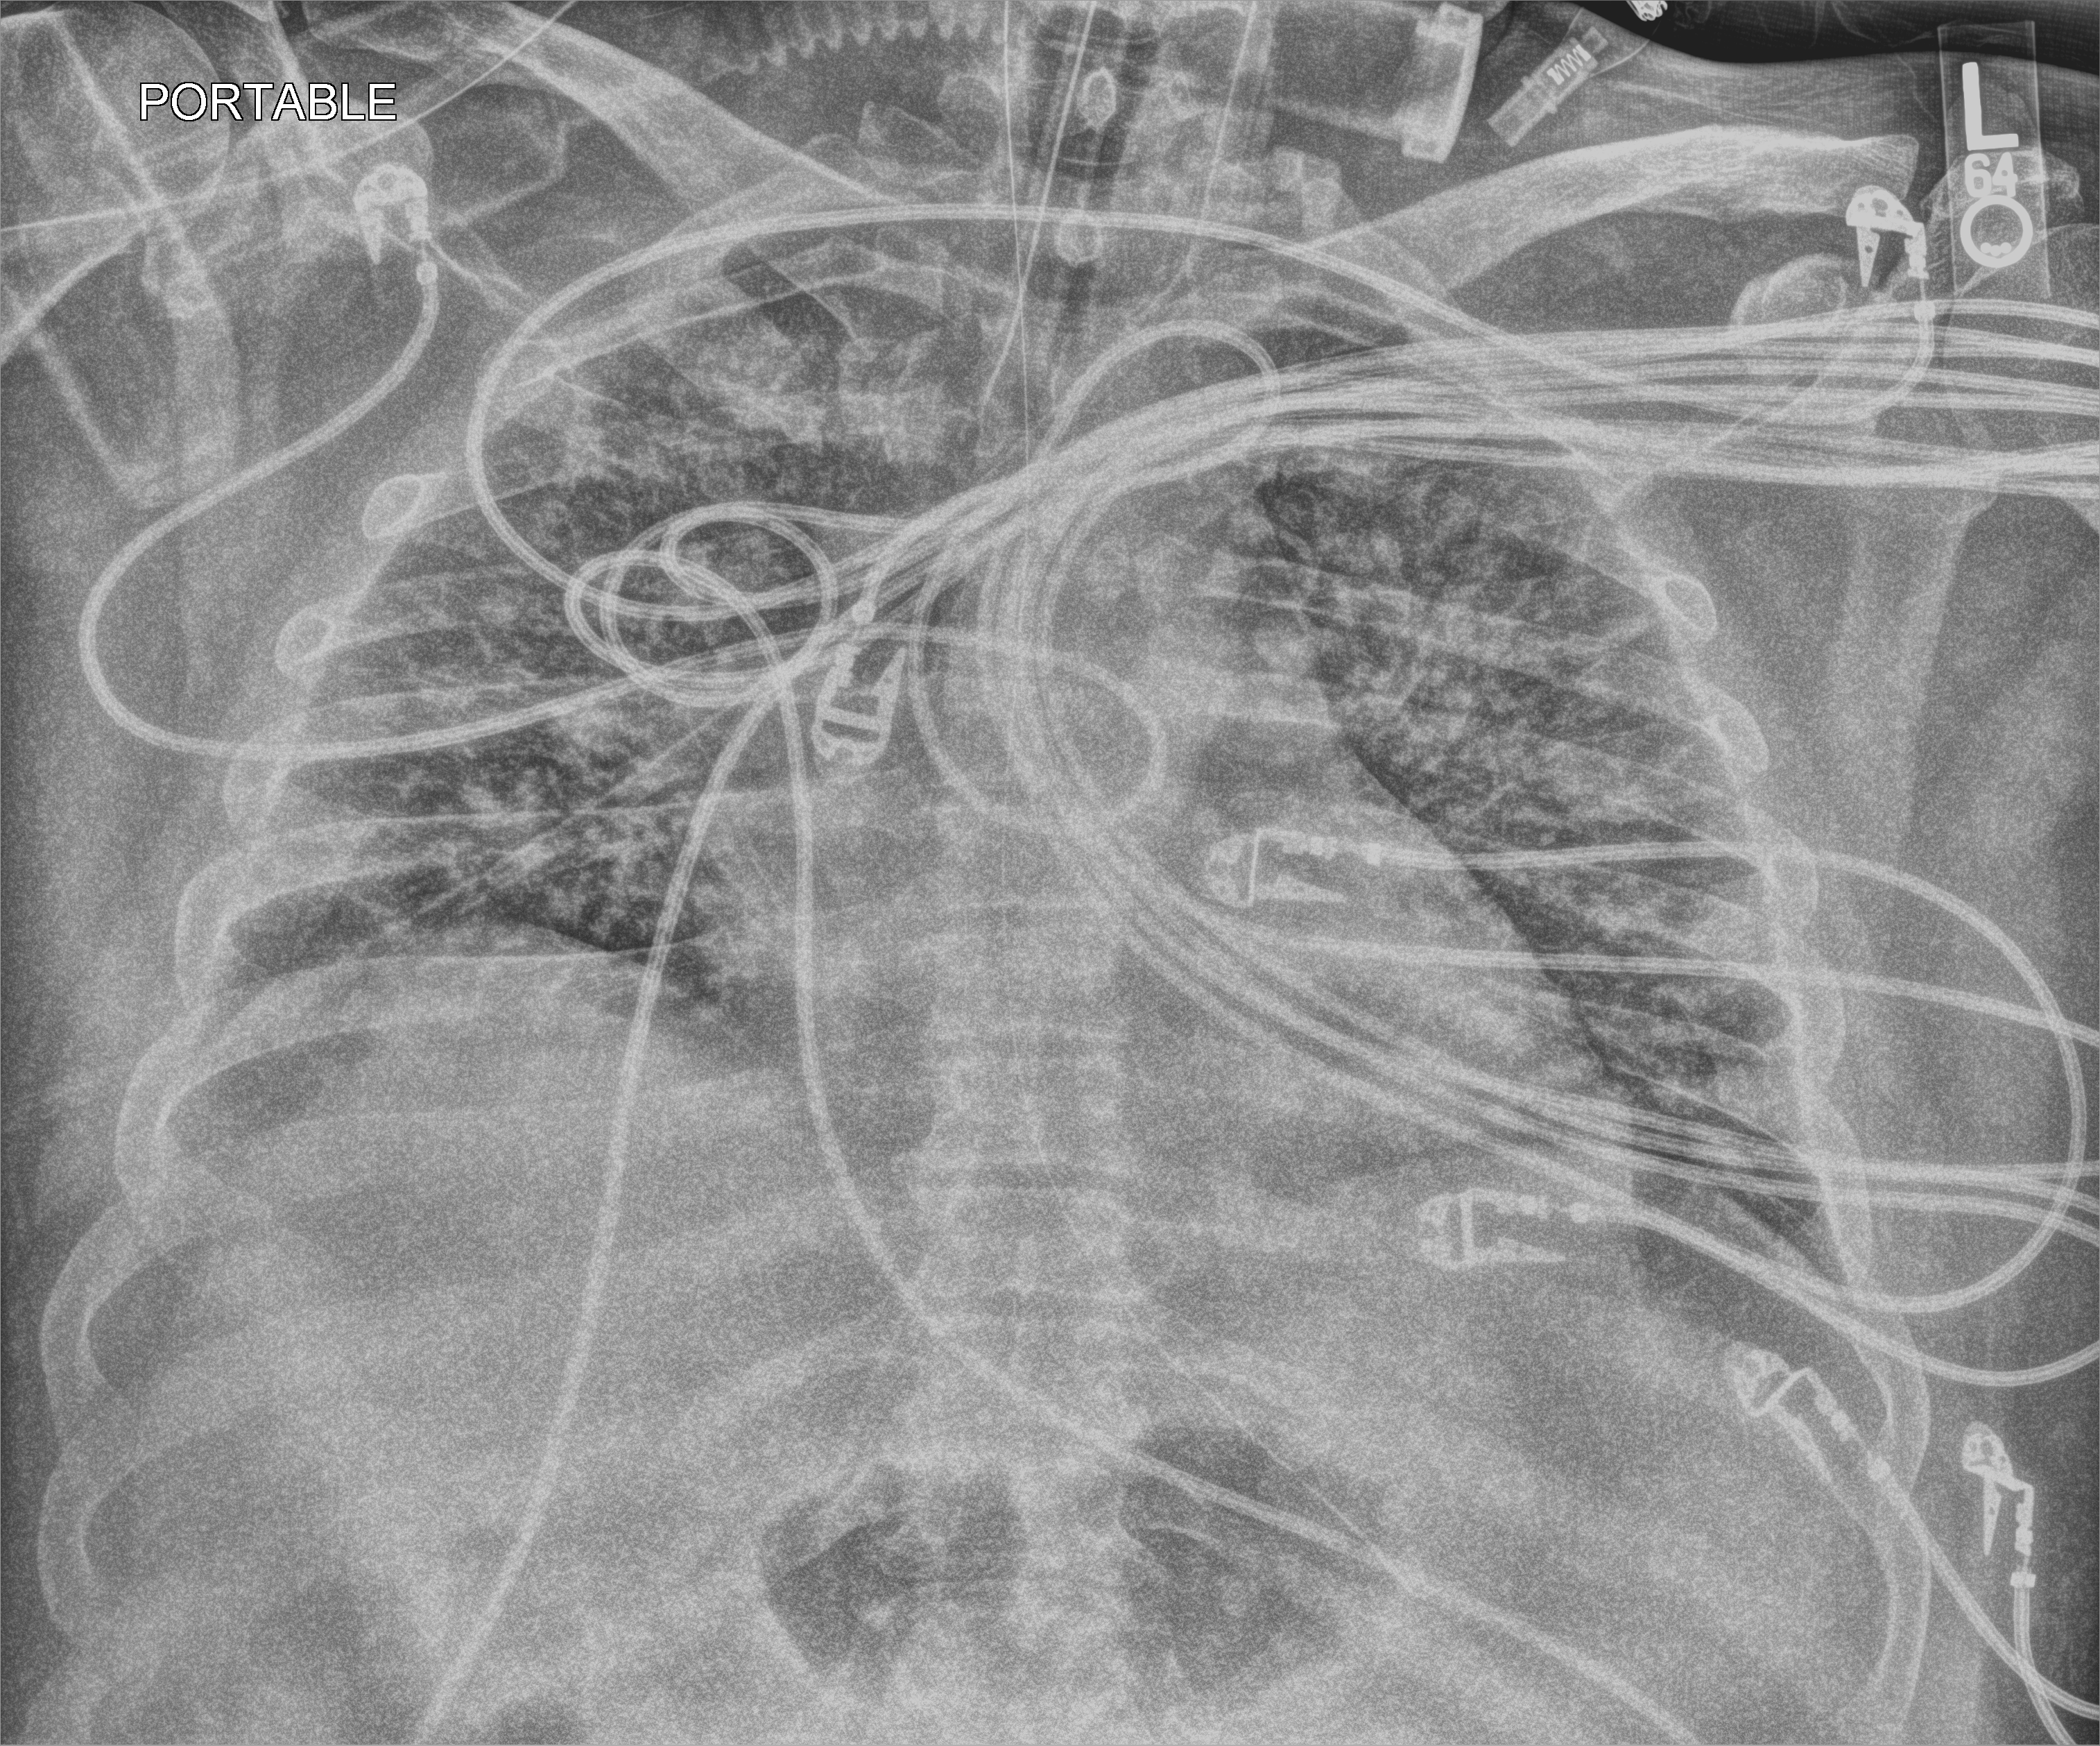
Bedside chest radiograph (computed radiography), anteroposterior (AP) projection. Adult patient hospitalised with COVID-19, age 18–59 years.
From the hospital-stay record, not from the radiograph (when in the stay this image was taken is not recorded):
- admitted to intensive care during this hospital stay: yes
- mechanically ventilated during this hospital stay: yes